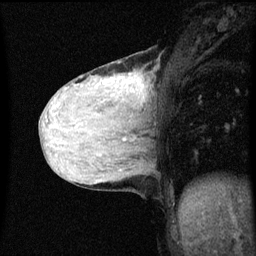
Breast MRI (dynamic contrast-enhanced), one sagittal slice. Position 24 of 60 along the scan axis. Dynamic contrast-enhanced series, image 2 of 3 at this slice position (ordered by acquisition). 1.5 T. TE 4.2 ms, TR 8.4 ms. 2 mm slice thickness. 256 × 256 image matrix, field of view 200 × 200 mm. Female patient, age 36 years.
Structures marked on this image (semi-automatically segmented with operator editing):
- analysis volume of interest (the breast-tissue region the enhancement analysis was run in; not a lesion): bounding box <48,56,159,151> (left, top, right, bottom; pixels)
- tumour enhancement mask (voxels above the 70 % enhancement threshold inside the analysis volume of interest): <130,74,145,99>